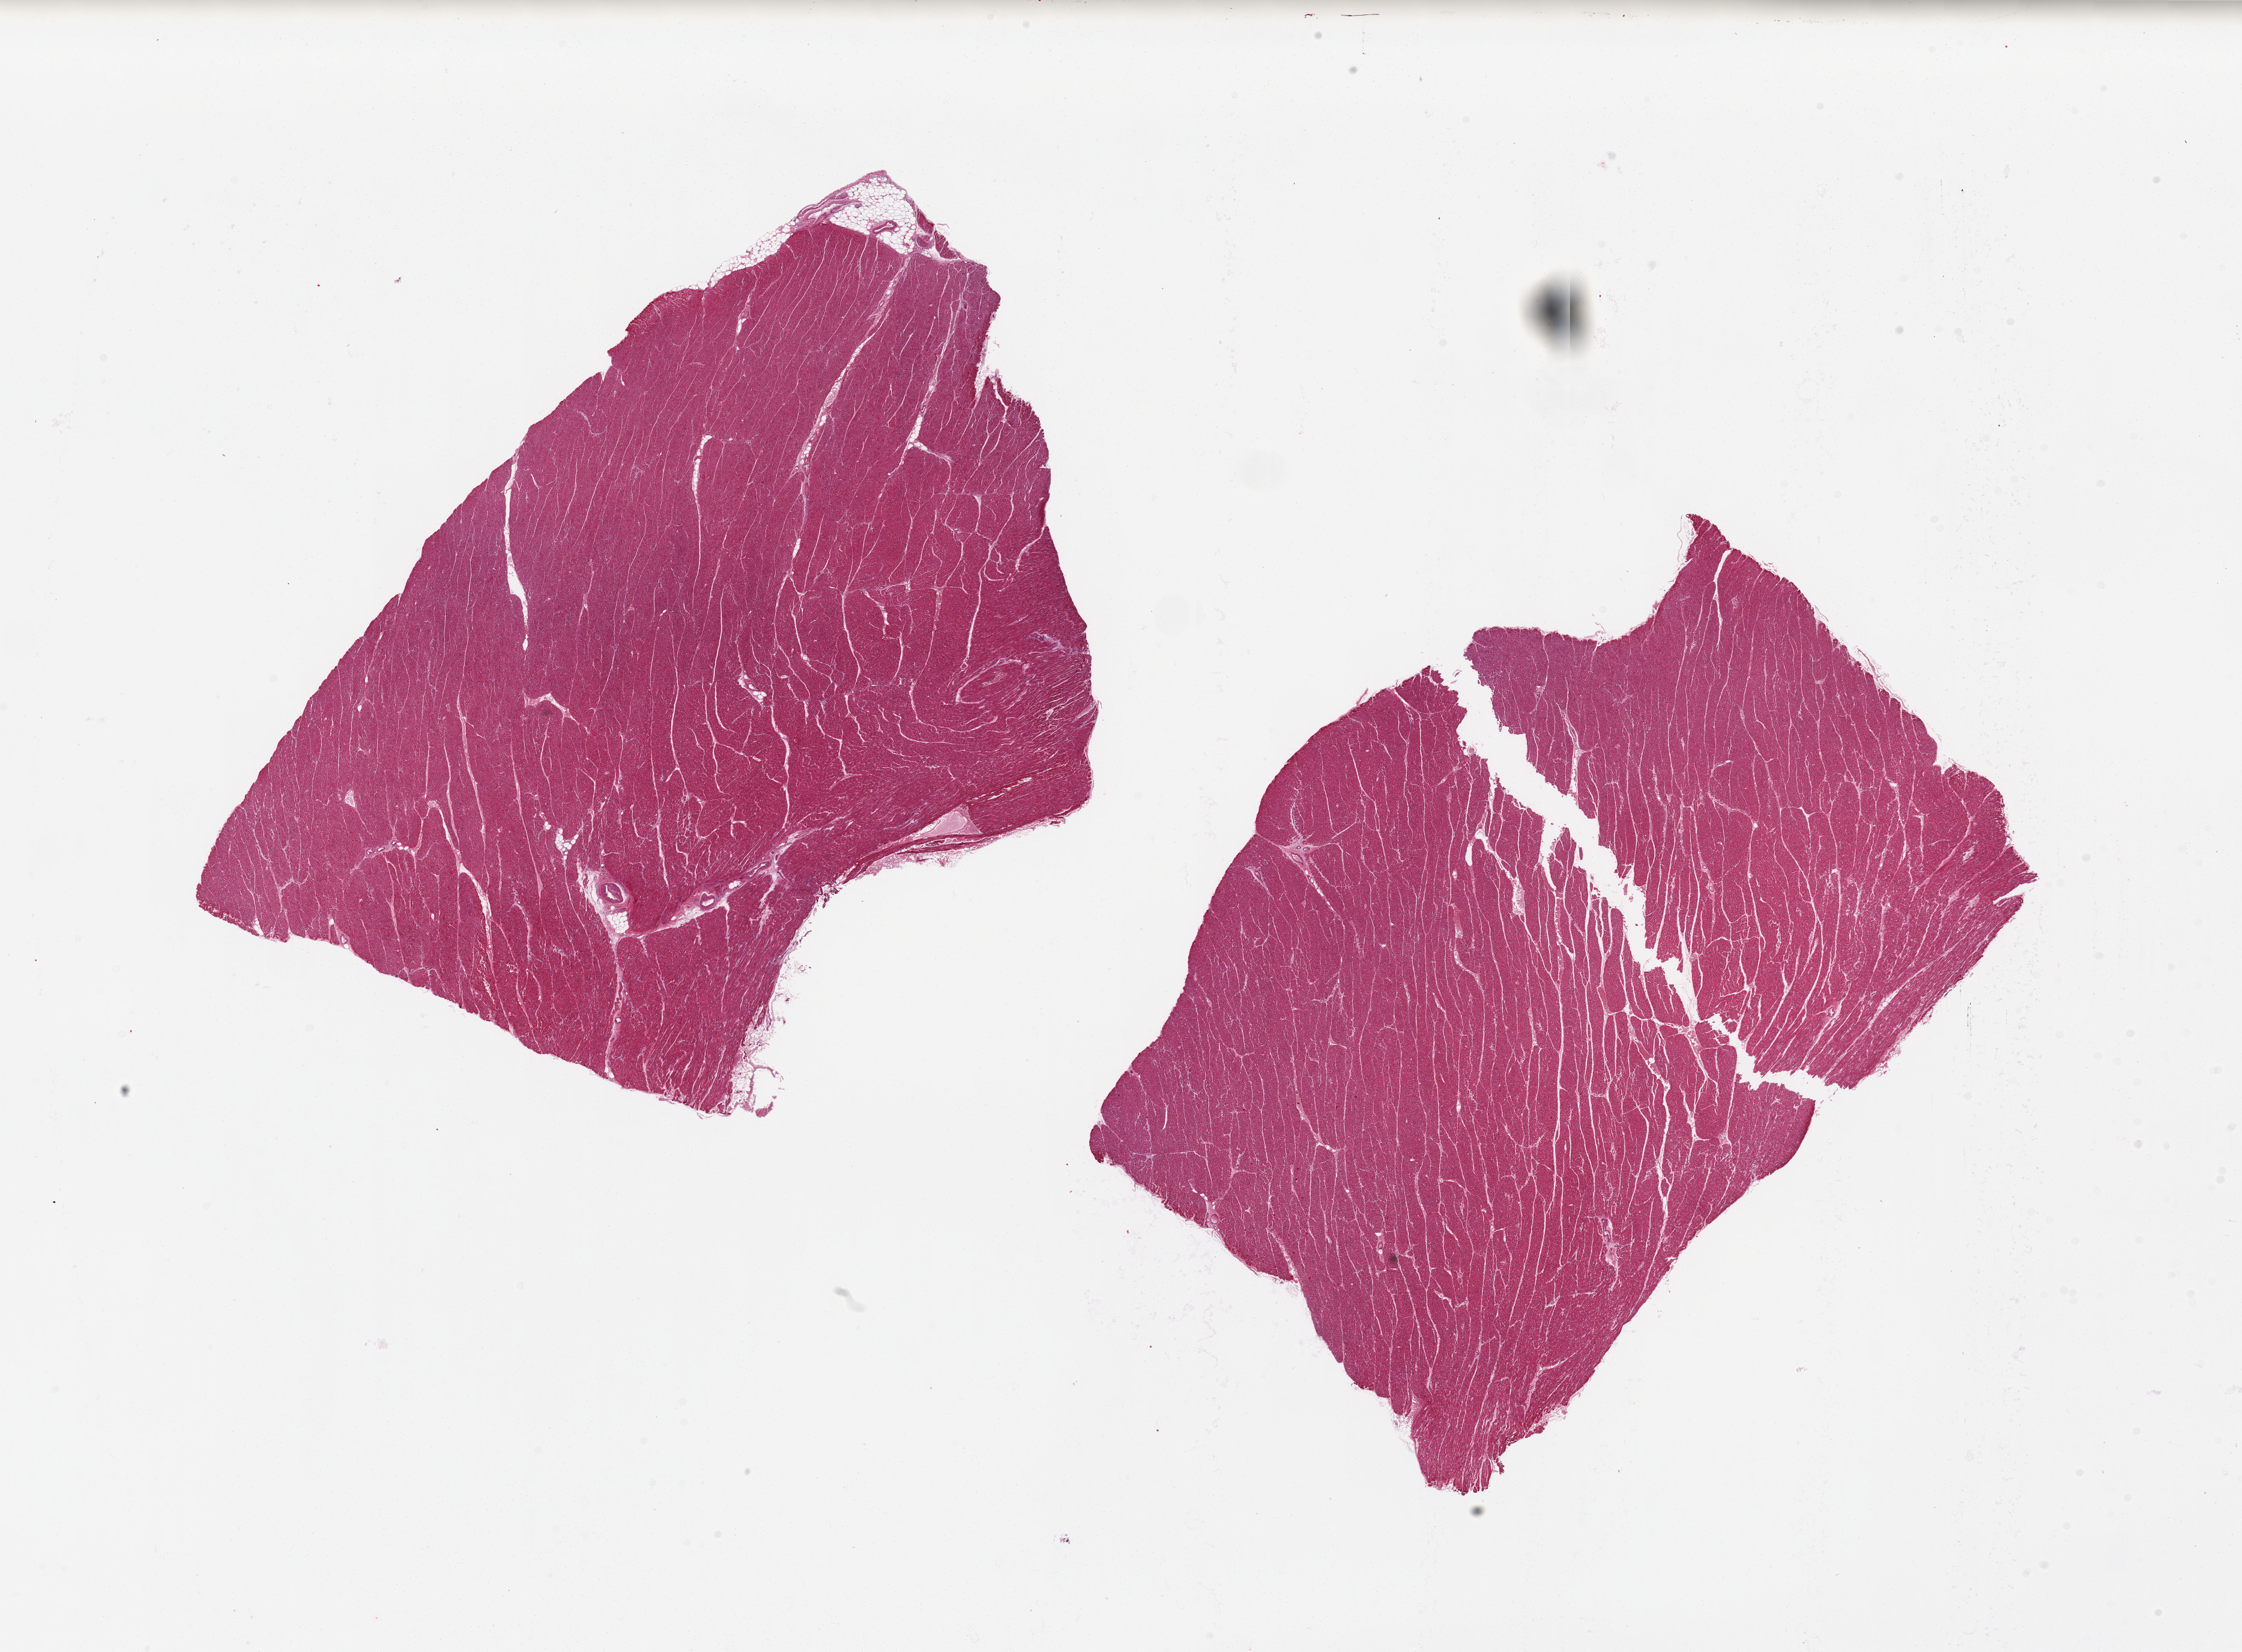
Whole-slide image, haematoxylin and eosin stain, whole scanned area (about 29.5 x 21.8 mm, from a 20x scan) shown as a low-resolution overview. PAXgene-fixed, paraffin-embedded tissue. Sampled site (target tissue): heart. Tissue donor sample. Donor sex: male.
Reviewer comment on this tissue sample: 2 pieces, 12x8.5 and 11x8mm; well trimmed.